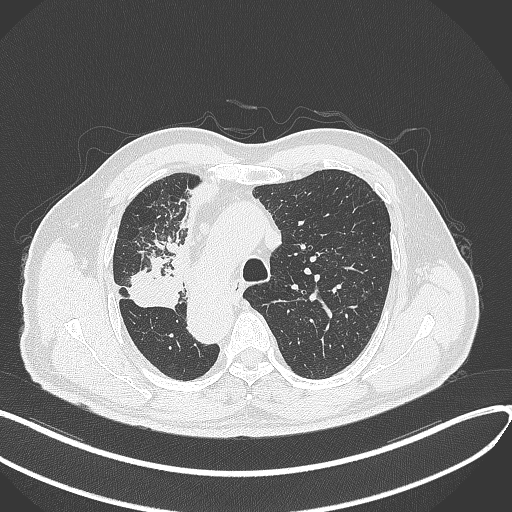
Chest CT, one axial slice. Slice 228 of 300 in the series (ordered by position). Reconstruction kernel B70f. 120 kVp. Lung window (W 1500 / L -600 HU). 1 mm slice thickness. 512 × 512 image matrix, field of view 400 × 400 mm. Male patient, age 67 years. From the clinical record (not read from this slice): clinical TNM (as recorded): T2a N0 M0.
Outlined on this slice (bounding box drawn by a radiologist):
- lung tumour (recorded histology: squamous cell carcinoma): bounding box (x1, y1, x2, y2) in pixels: (127, 257, 188, 312)